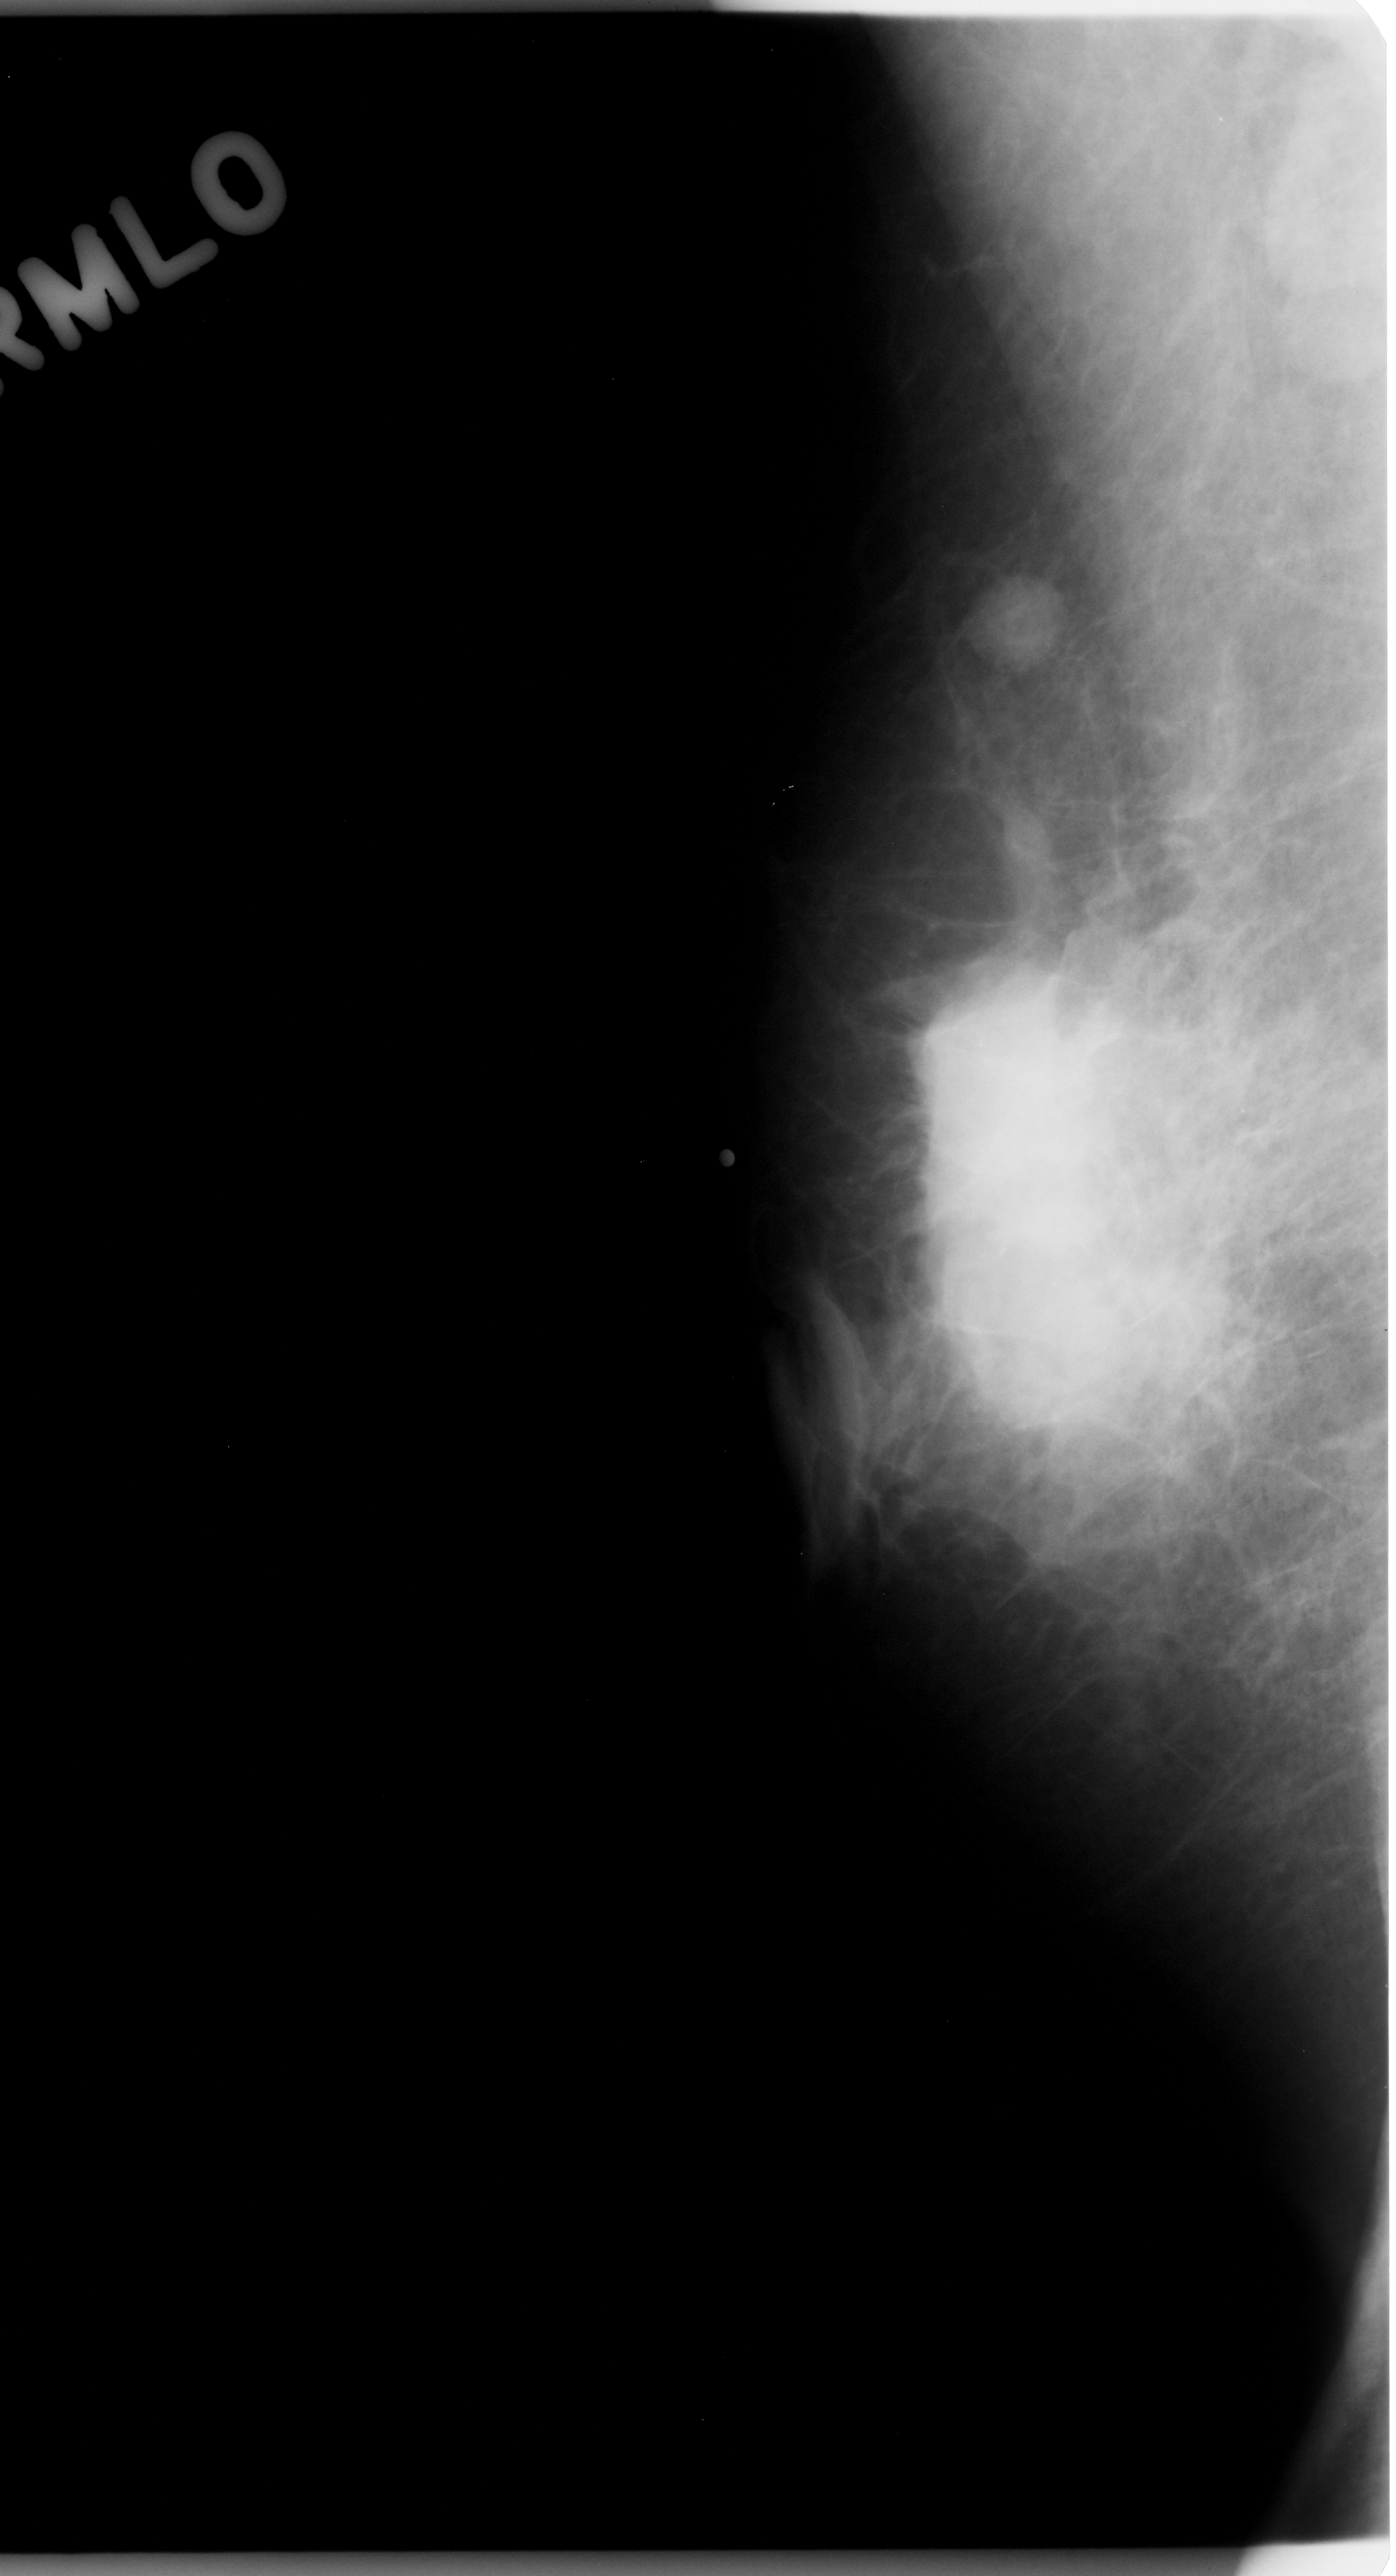
Mammogram (digitized film); right breast; MLO view; BI-RADS breast density category 3 (scale 1–4); 1396 × 2576 image matrix.
Expert-marked regions of interest on this film, with their recorded descriptors:
- mass, shape round, margins circumscribed; BI-RADS assessment category 5; subtlety rating 5 on a 1 (subtle) to 5 (obvious) scale; pathology result (as recorded, not read from the image): malignant: bounding box (x1, y1, x2, y2) in pixels: (956, 560, 1109, 675)